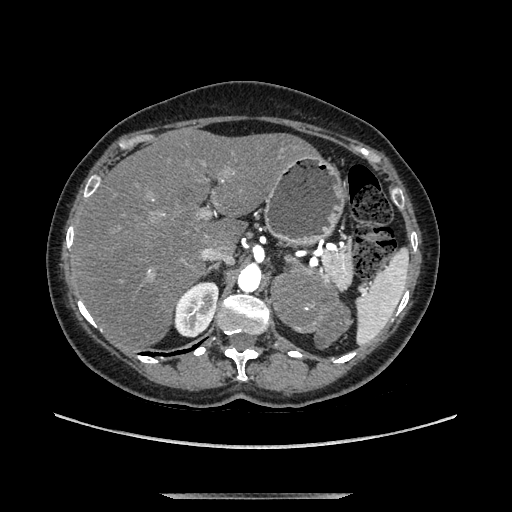
Contrast-enhanced abdominal CT, one axial slice; soft-tissue window (W 400 / L 40 HU); 512 × 512 image matrix, field of view 400 × 400 mm. Female patient. From the clinical record (not read from this slice): diagnosis: adrenocortical carcinoma; tumour side: left adrenal; tumour size at pathology: 9 cm; Ki-67 index: 2 %; stage (as recorded): 3.
Outlined on this slice (semi-automatic segmentation, software-assisted and operator-edited):
- mass: bounding box [x1, y1, x2, y2] px = [274, 257, 349, 347]